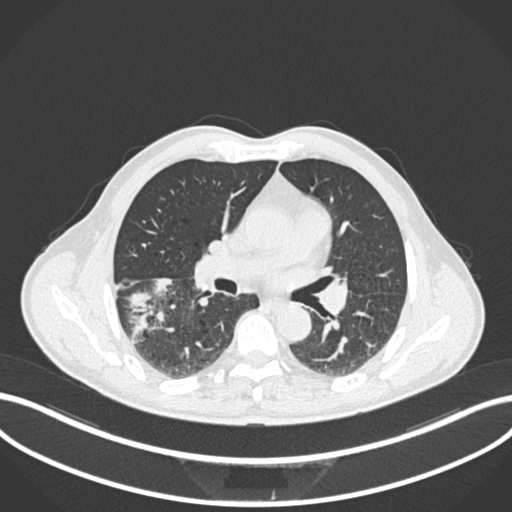
Chest CT, one axial slice. Position 108 of 208 along the scan axis. Reconstruction kernel B30f. 120 kVp. Lung window (W 1500 / L -600 HU). 512 × 512 image matrix, field of view 400 × 400 mm. Male patient, age 58 years. Case-level facts recorded for this patient, not image findings: clinical TNM (as recorded): T3 N0 M0.
Annotated regions visible in this slice (bounding box drawn by a radiologist):
- lung tumour (recorded histology: squamous cell carcinoma): bounding box <127,272,187,346> (left, top, right, bottom; pixels)